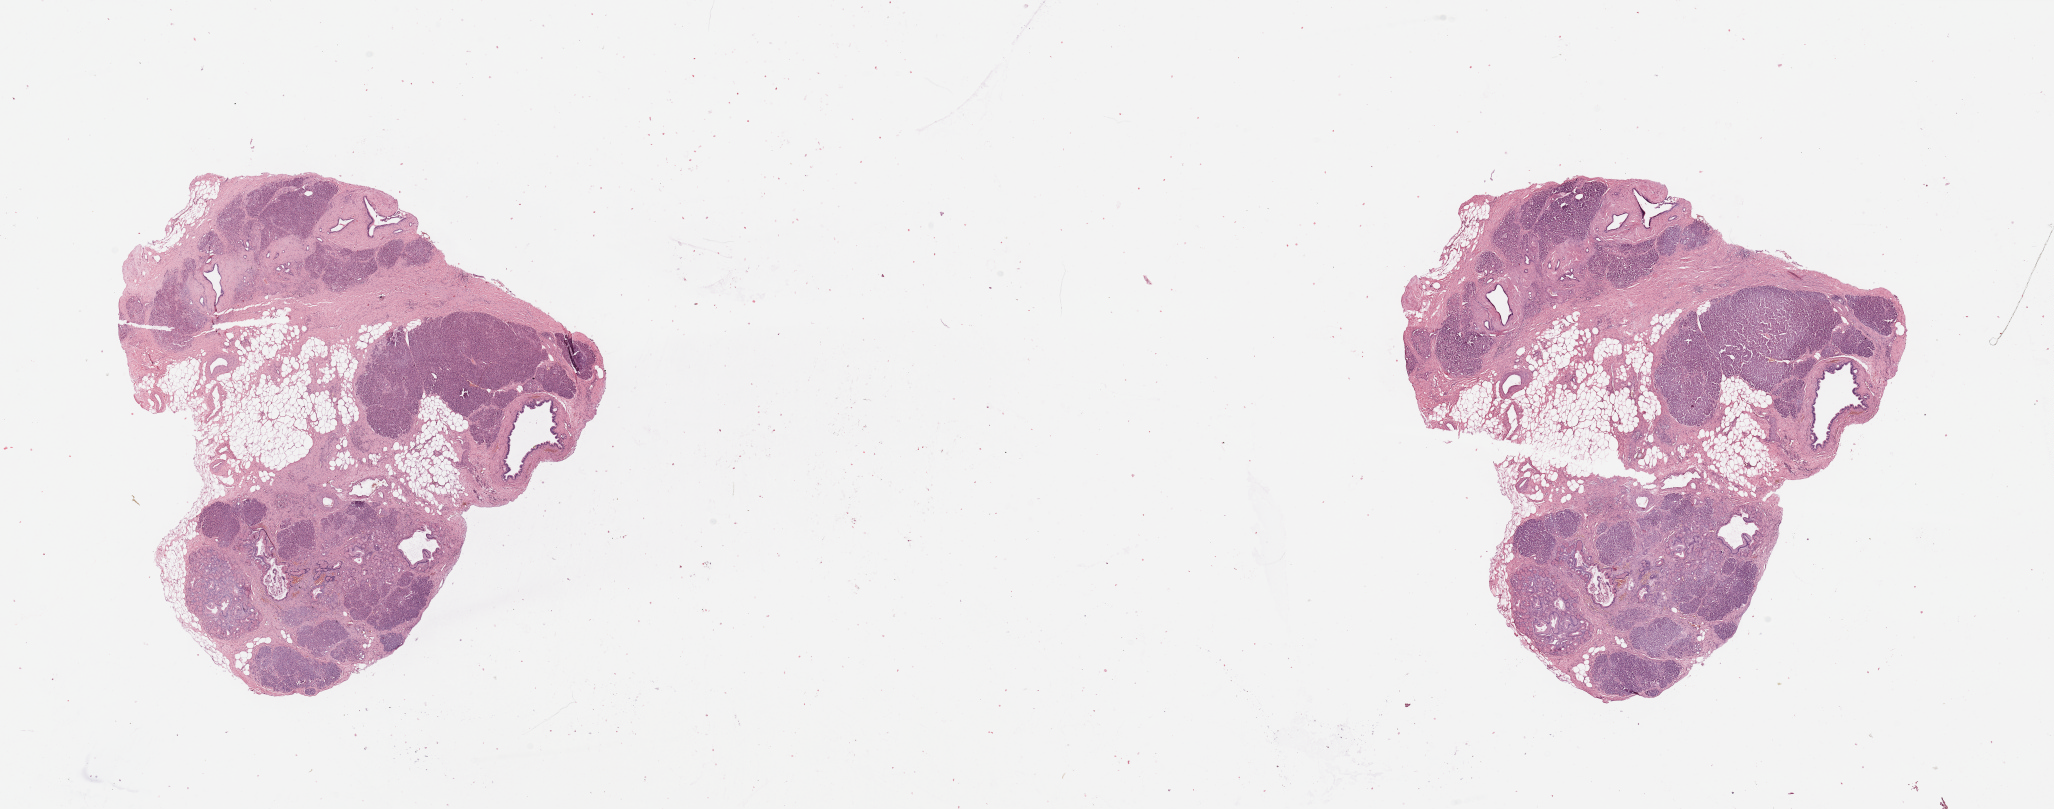
Whole-slide histology image, H&E-stained — a low-resolution overview of the entire scanned area, about 32.5 x 12.8 mm, pancreas, tissue type not recorded.
- patient diagnosis (cohort enrolment): ductal adenocarcinoma (pancreas)